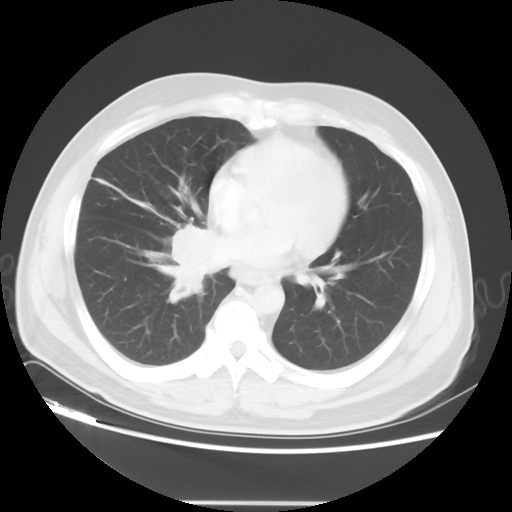
Chest CT, one axial slice. Position 20 of 48 along the scan axis. Reconstruction kernel STANDARD. Lung window (W 1500 / L -600 HU). 5 mm slice thickness. 512 × 512 image matrix, field of view 390 × 390 mm. Male patient, age 53 years. From the clinical record (not read from this slice): clinical TNM (as recorded): T2 N3 M0; histopathological grade: G3.
Structures marked on this image (rectangle marked by the reading radiologist):
- lung tumour (recorded histology: small cell carcinoma): bounding box (x1, y1, x2, y2) in pixels: (160, 223, 216, 298)